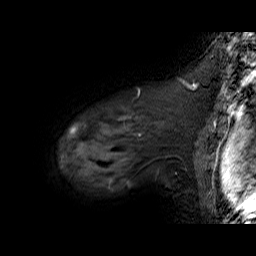
Breast MRI (dynamic contrast-enhanced), one sagittal slice. Position 54 of 60 along the scan axis. Dynamic contrast-enhanced series, time point 2 of 6 at this slice position (early post-contrast). 1.5 T. TE 6.3 ms, TR 32.9 ms. 256 × 256 image matrix, field of view 200 × 200 mm. Female patient. From the clinical record (not read from this slice): setting: breast cancer imaged before/during neoadjuvant chemotherapy; receptor status: HER2-positive.
Structures marked on this image (semi-automatically segmented with operator editing):
- analysis volume of interest (the breast-tissue region the enhancement analysis was run in; not a lesion): bounding box [x1, y1, x2, y2] px = [60, 92, 195, 174]
- tumour enhancement mask (voxels above the 100 % enhancement threshold inside the analysis volume of interest): [70, 127, 76, 133]